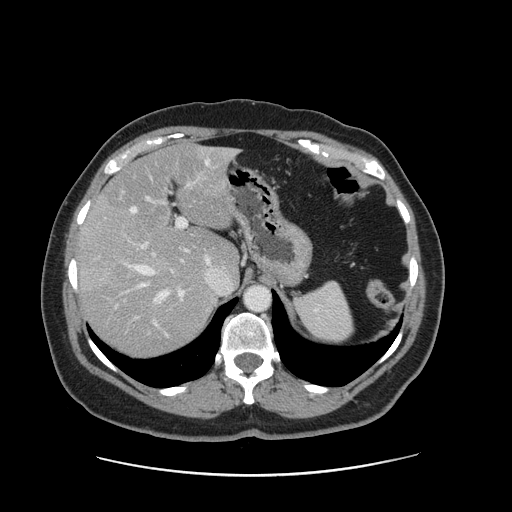
Contrast-enhanced abdominal CT, one axial slice; position 107 of 161 along the scan axis; soft-tissue window (W 400 / L 40 HU); 2.5 mm slice thickness; 512 × 512 image matrix. Female patient, age 62 years. From the clinical record (not read from this slice): diagnosis: colorectal cancer liver metastases, imaged before liver resection; multiple liver metastases: no; largest metastasis: 2.5 cm; chemotherapy before resection: yes.
Annotated regions visible in this slice (expert manual segmentation):
- hepatic veins: bounding box <130,160,231,301> (left, top, right, bottom; pixels)
- liver: <80,145,238,356>
- planned liver remnant (the part of the liver to remain after resection): <100,146,238,277>
- portal vein (with intrahepatic branches): <114,171,203,309>
- liver metastasis: <108,262,131,290>